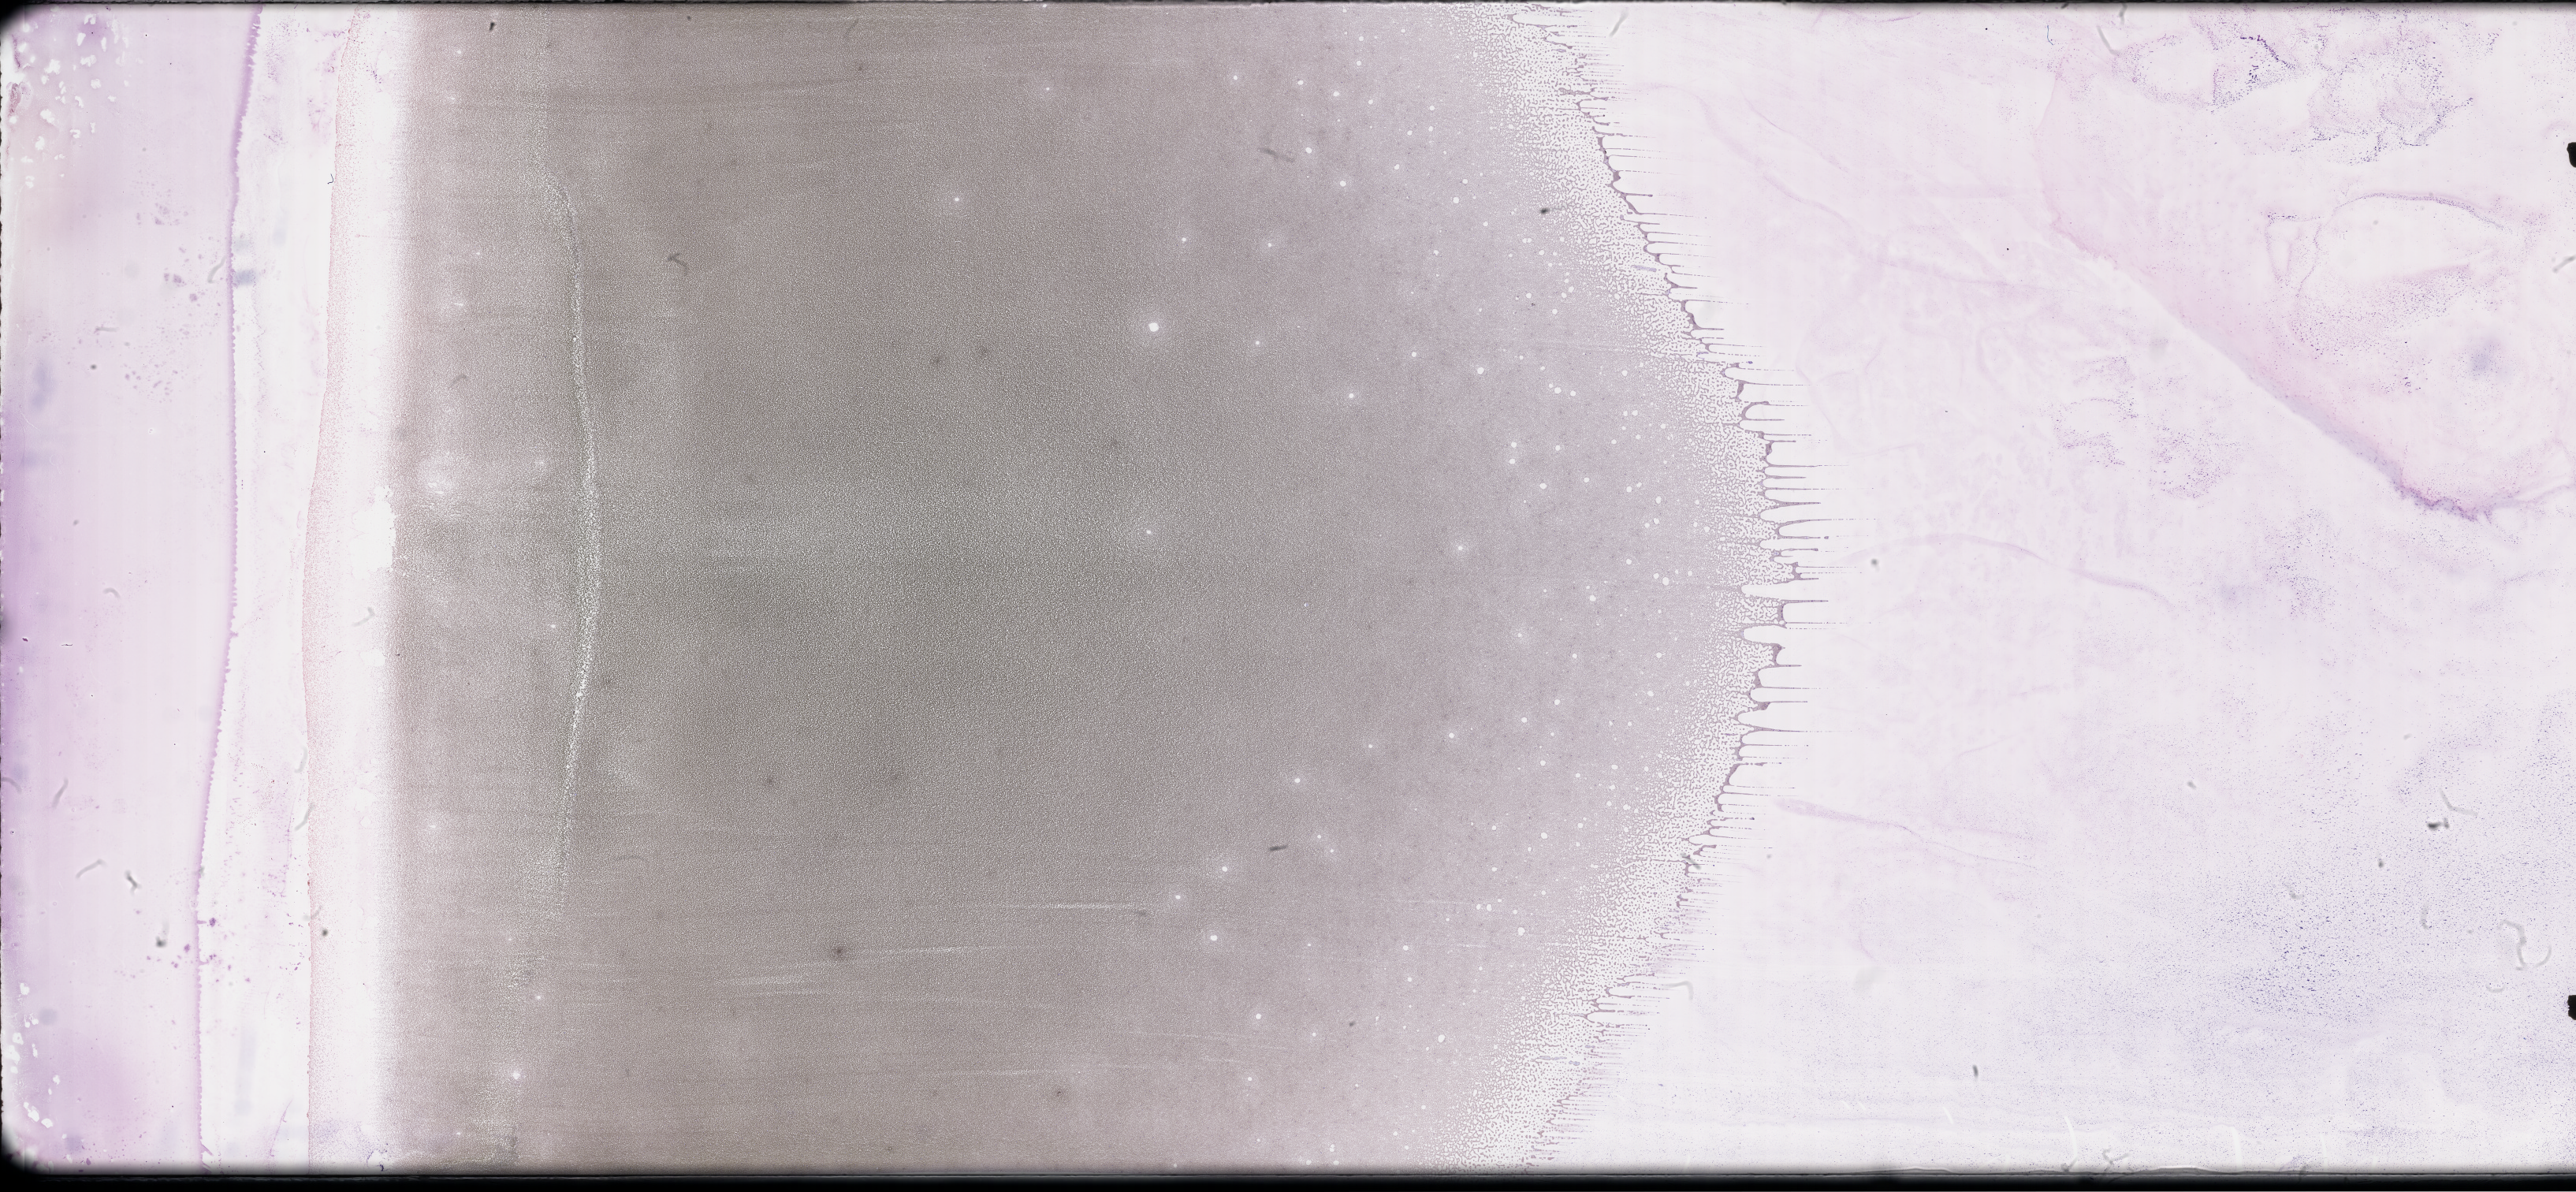
Wright-Giemsa-stained whole blood smear, whole-slide image — a low-resolution overview of the entire scanned area, about 52.8 x 24.4 mm, smear from an EDTA sample, specimen time point: collected on treatment. Patient: male.
Patient diagnosis: Plasma Cell Myeloma.